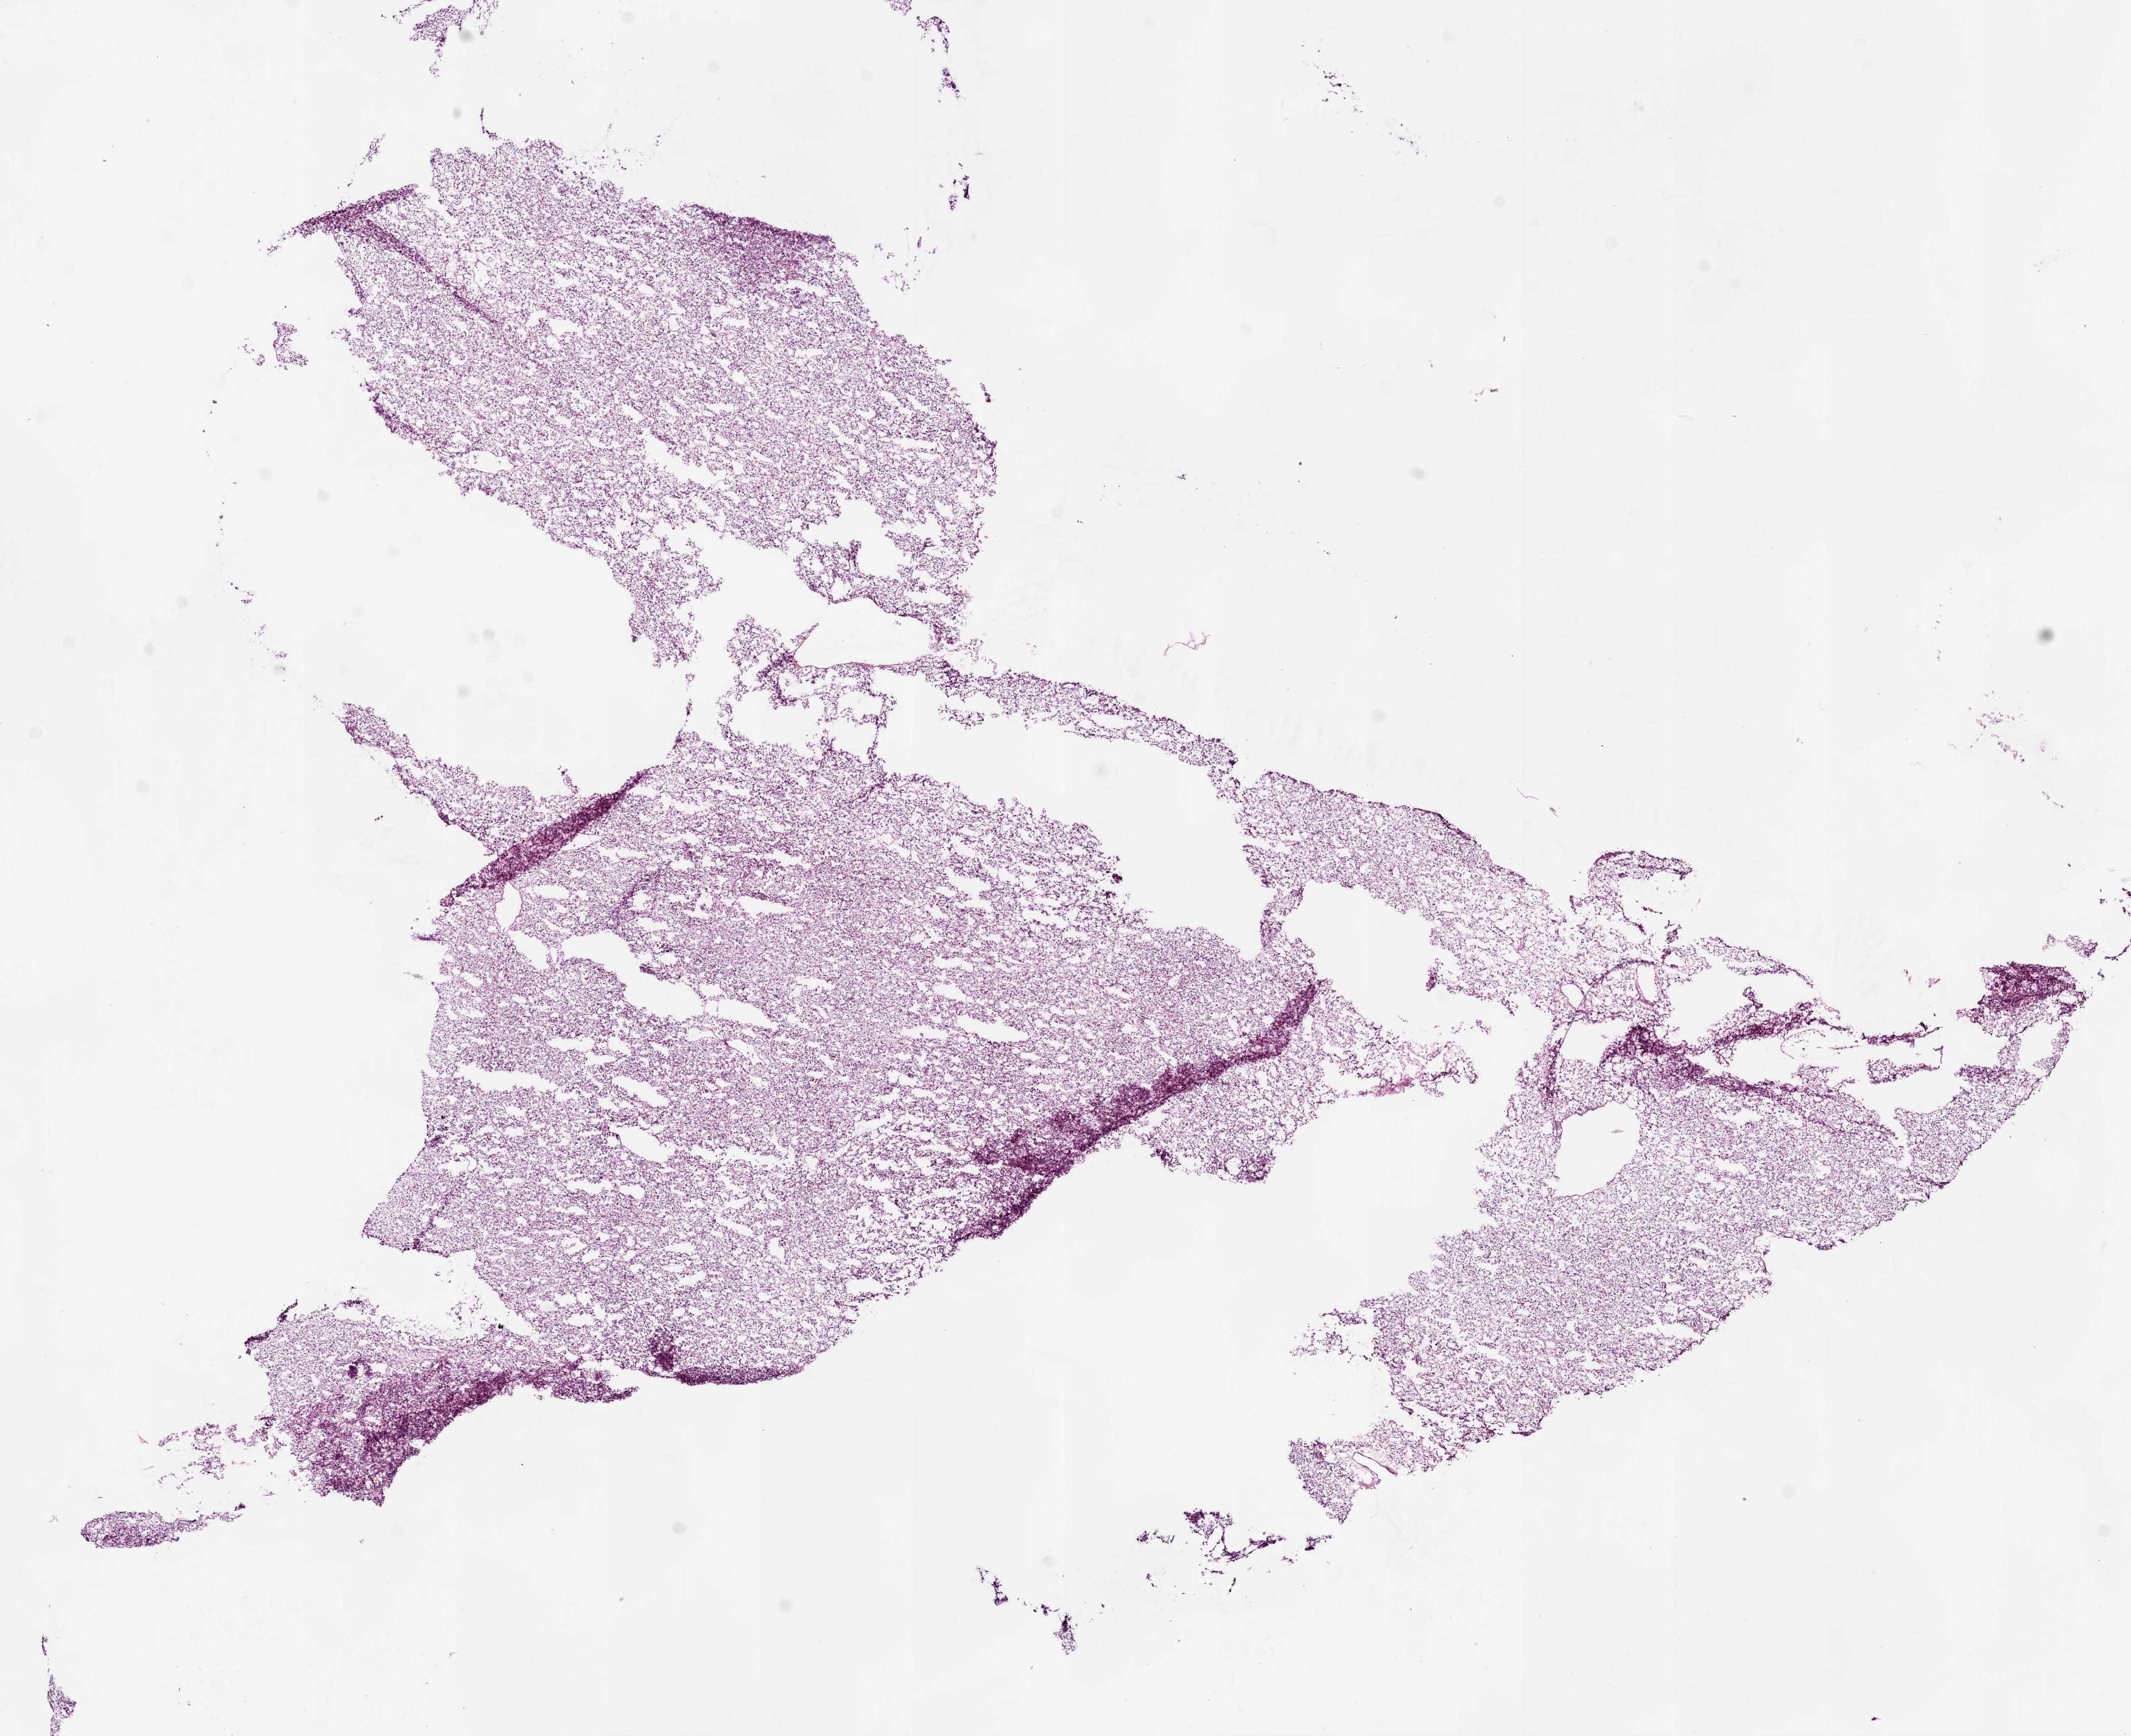
Digitized Hematoxylin and eosin (H&E) stained tissue section (whole slide) — a low-resolution overview of the entire scanned area, about 14.0 x 11.4 mm (from a 20x scan). Frozen section from the bottom of the tissue portion. Primary tumour sample from the kidney. Patient: female, age at initial diagnosis 59 years. Histologic grade: G2 (moderately differentiated). Pathologist review of this section (percent, as recorded): tumour cells 95%, tumour nuclei 90%, normal cells 0%, stromal cells 5%, necrosis 0%.
AJCC pathologic stage: I. Histologic diagnosis: Clear cell adenocarcinoma, NOS.